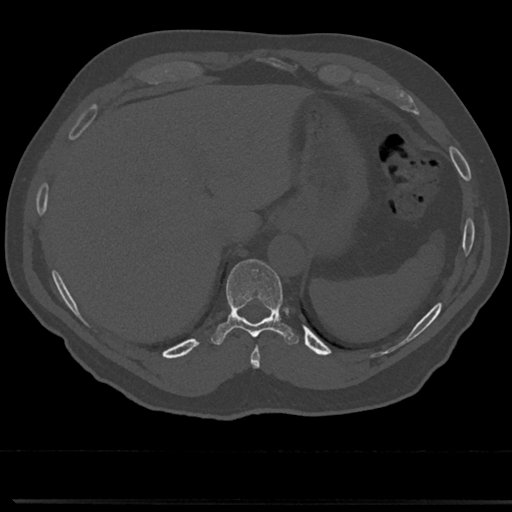
CT including the spine, one axial slice; position 258 of 817 along the scan axis; reconstruction kernel Br40s/3; bone window (W 1800 / L 400 HU); 0.5 mm slice thickness; 512 × 512 image matrix, field of view 355 × 355 mm. Male patient, age 61 years. Case-level facts recorded for this patient, not image findings: primary cancer: prostate.
Annotated regions visible in this slice (semi-automatic segmentation, software-assisted and operator-edited):
- T10 vertebra: box from (x=211, y=260) to (x=299, y=345) px
- T9 vertebra: (x=251, y=332)–(x=263, y=366)